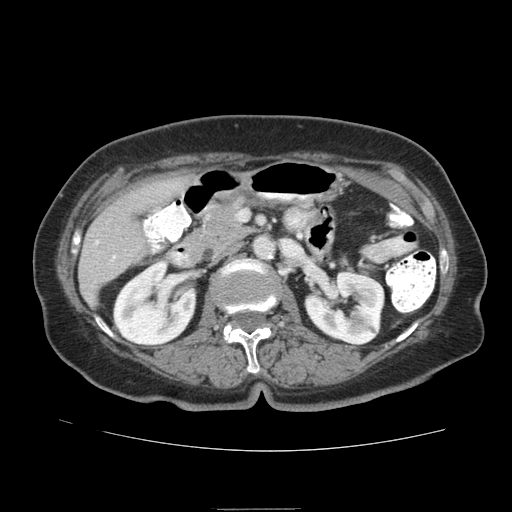
Contrast-enhanced abdominal CT (liver protocol), one axial slice. Position 32 of 95 along the scan axis. Reconstruction kernel STANDARD. 140 kVp. Soft-tissue window (W 400 / L 40 HU). 2.5 mm slice thickness. 512 × 512 image matrix, field of view 360 × 360 mm. Case-level facts recorded for this patient, not image findings: diagnosis: hepatocellular carcinoma (patient treated with transarterial chemoembolisation; whether this scan precedes or follows treatment is not stated here); TNM stage (as recorded): Stage-IVA; Child-Pugh class: B; tumour nodularity: uninodular.
Annotated regions visible in this slice (semi-automatic segmentation, software-assisted and operator-edited):
- liver parenchyma outside the tumour (the mass and vessels are separate outlines, so this box may not span the whole liver): box from (x=78, y=176) to (x=198, y=304) px
- liver vessels: (x=96, y=240)–(x=116, y=259)